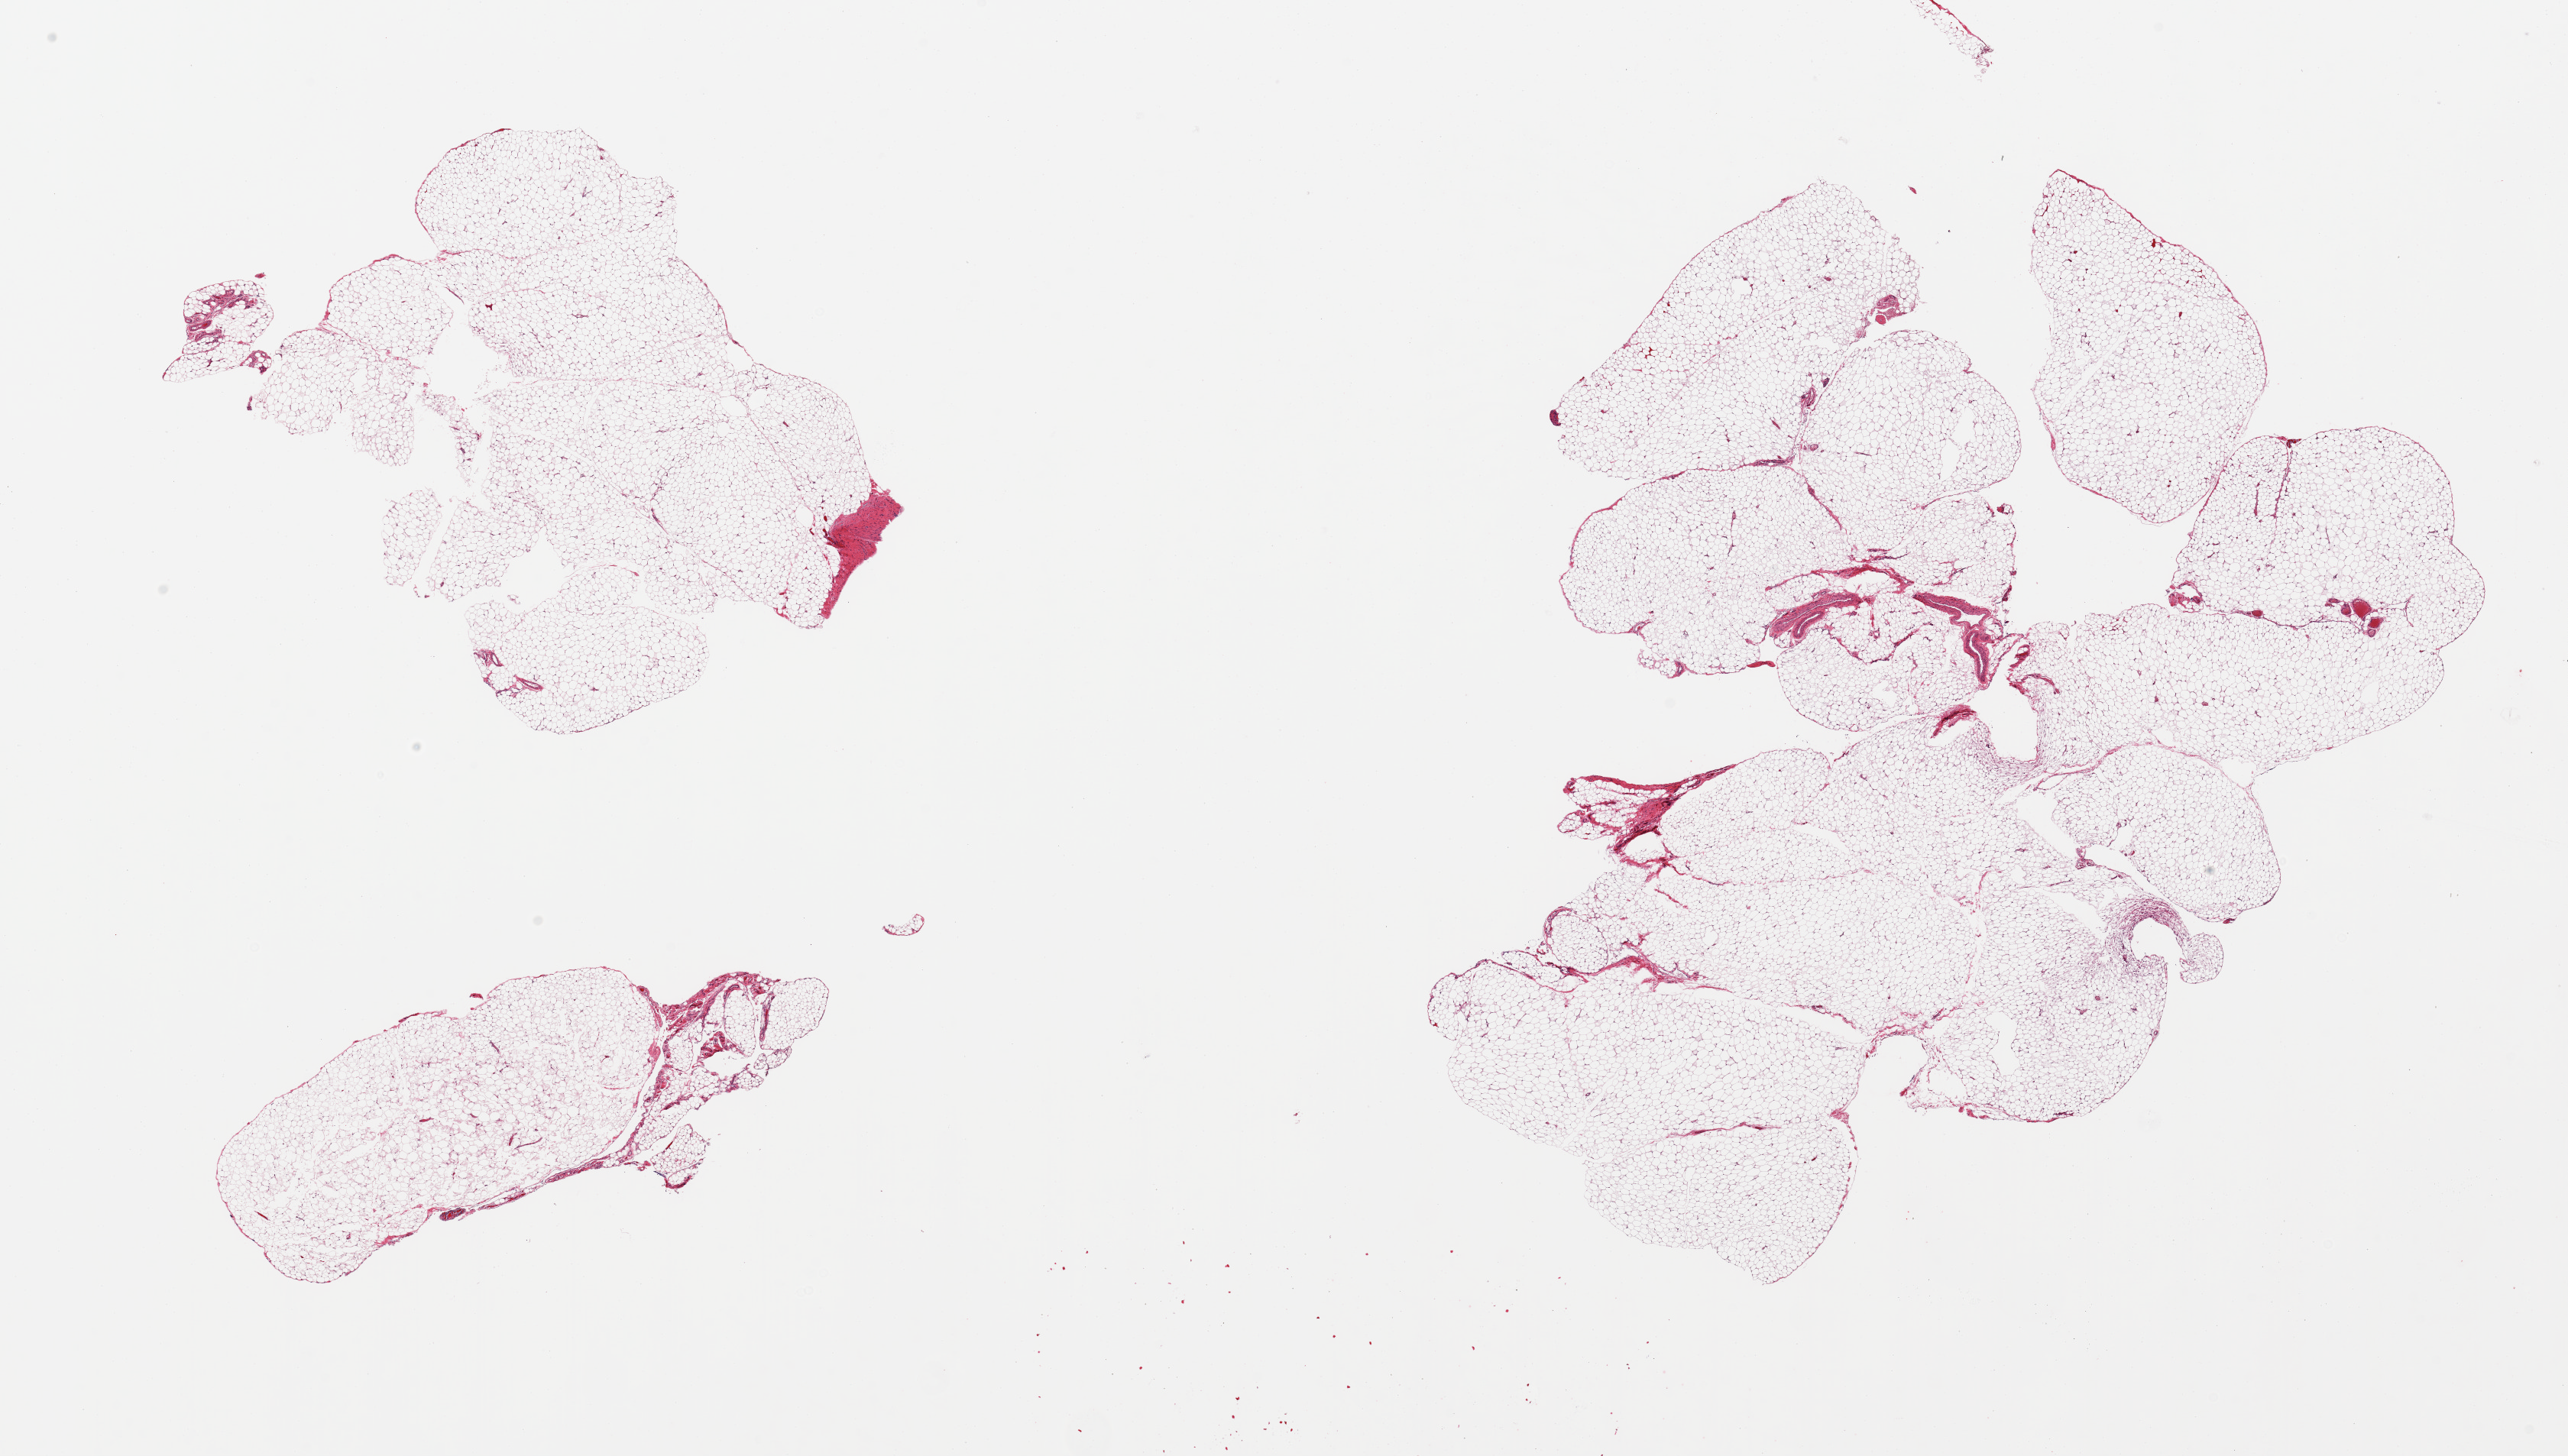
Digitized H&E-stained section, a low-resolution overview of the entire scanned area, about 26.6 x 15.1 mm (slide scanned at 20x). PAXgene-fixed, paraffin-embedded tissue. Section of omentum (target tissue). Donor tissue sample. Donor: female.
Review note (as recorded): 2 fragmented pieces; lobulated mature adipose tissue with scant fibrovascular component.